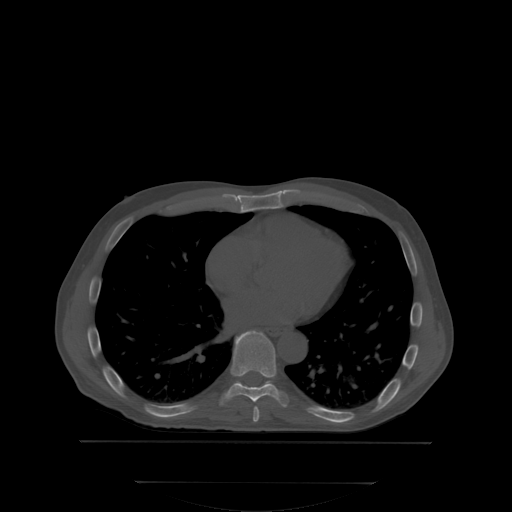
CT including the spine, one axial slice; slice 215 of 350 in the series (ordered by position); bone window (W 1800 / L 400 HU); 2.5 mm slice thickness; 512 × 512 image matrix. Patient: male, 58 years. From the clinical record (not read from this slice): primary cancer: prostate; vertebrae with lytic lesions (as recorded): L1.
Outlined on this slice (semi-automatically segmented with operator editing):
- T7 vertebra: bounding box (x1, y1, x2, y2) in pixels: (253, 408, 259, 421)
- T8 vertebra: (221, 331, 288, 404)